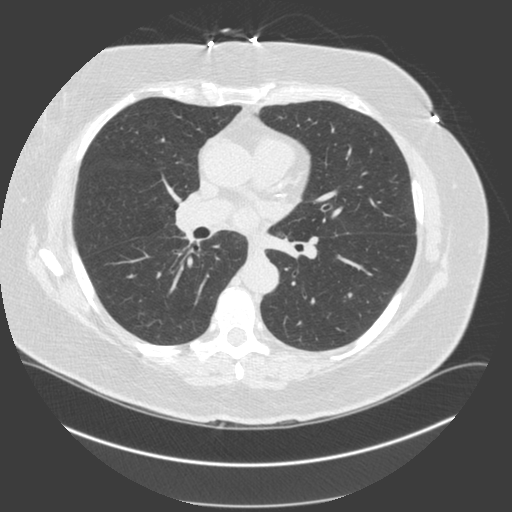
Axial slice from a low-dose chest CT screening exam, second screening round (one year after baseline), lung window (W 1500 / L -600 HU), 2 mm slice thickness, slice 74 of 179 in the series, 512 × 512 image matrix, field of view 400 × 400 mm. Female, age 66 years at enrolment. Current smoker at enrolment.
Expert-annotated lung lesion, bounding box [x1, y1, x2, y2] px = [332, 283, 369, 313]. No non-calcified nodule or mass ≥4 mm was recorded by the screening reader at this exam. Official screen result: negative screen, minor abnormalities not suspicious for lung cancer. Participant outcome: lung cancer diagnosed 495 days after this screen (after the third annual screen) — non-small cell carcinoma, left lower lobe, poorly differentiated (G3), stage IA (AJCC 6th edition), 20 mm at pathology.